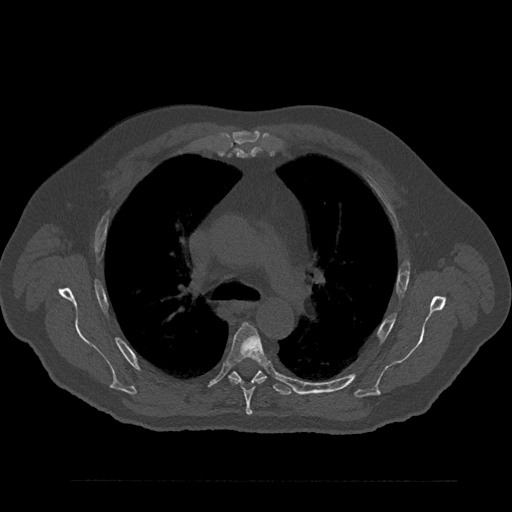
CT including the spine, one axial slice; slice 587 of 797 in the series (ordered by position); 120 kVp; bone window (W 1800 / L 400 HU); 512 × 512 image matrix, field of view 430 × 430 mm. Patient: male, 61 years. Case-level facts recorded for this patient, not image findings: primary cancer: prostate.
Structures marked on this image (semi-automatically segmented with operator editing):
- T5 vertebra: bounding box (x1, y1, x2, y2) in pixels: (227, 323, 266, 415)
- T6 vertebra: (229, 364, 292, 396)